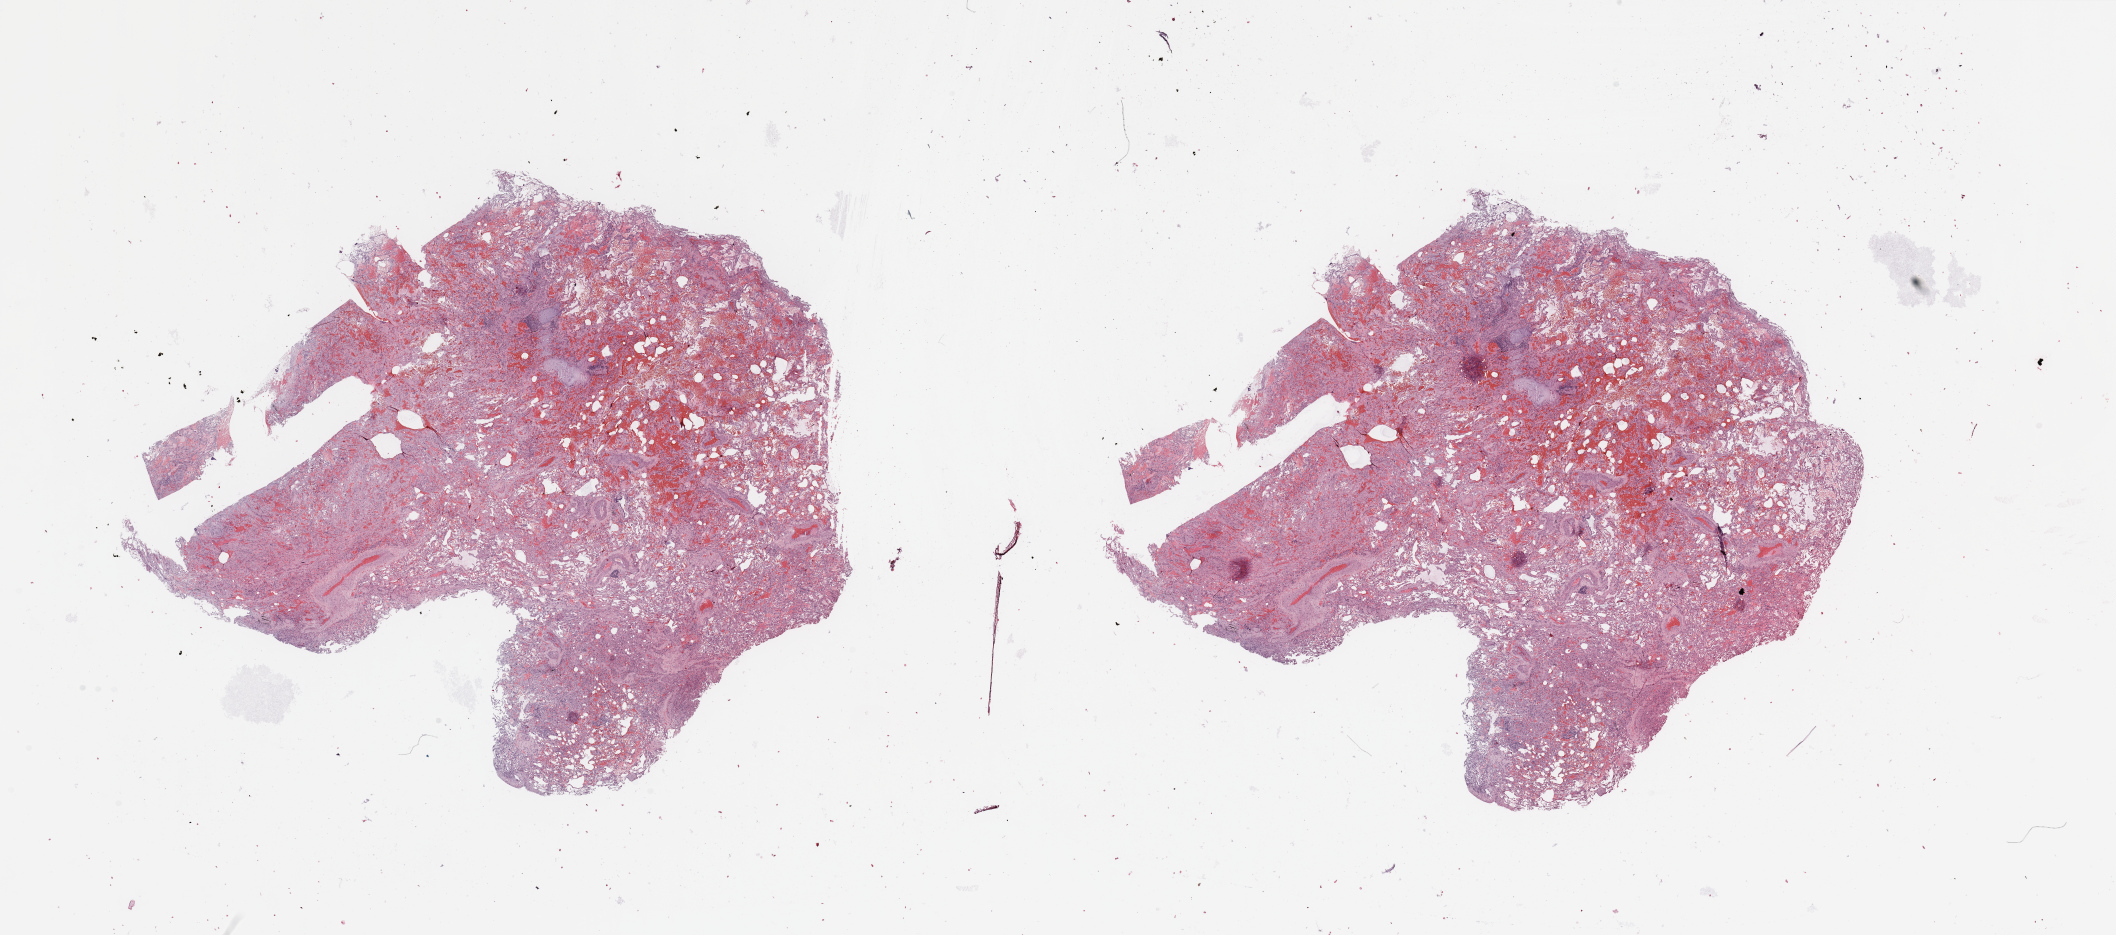
Whole-slide histology image, H&E, low-resolution overview of the scanned area, about 33.5 x 14.8 mm; normal (non-tumour) tissue sample, lung. Patient: male, age 39 years.
* this section: normal (non-tumour) tissue from the same patient
* patient diagnosis: Adenocarcinoma, NOS